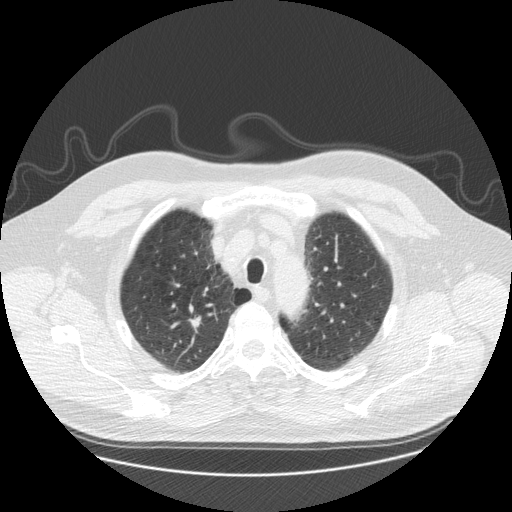
Low-dose screening chest CT, one axial slice; position 143 of 173 along the scan axis; reconstruction kernel STANDARD; lung window (W 1500 / L -600 HU); 2.5 mm slice thickness; 512 × 512 image matrix, field of view 400 × 400 mm.
Annotated regions visible in this slice (outlined manually by an expert reader):
- lesion 1 (tumor, upper lobe of right lung): bounding box <189,316,201,332> (left, top, right, bottom; pixels)